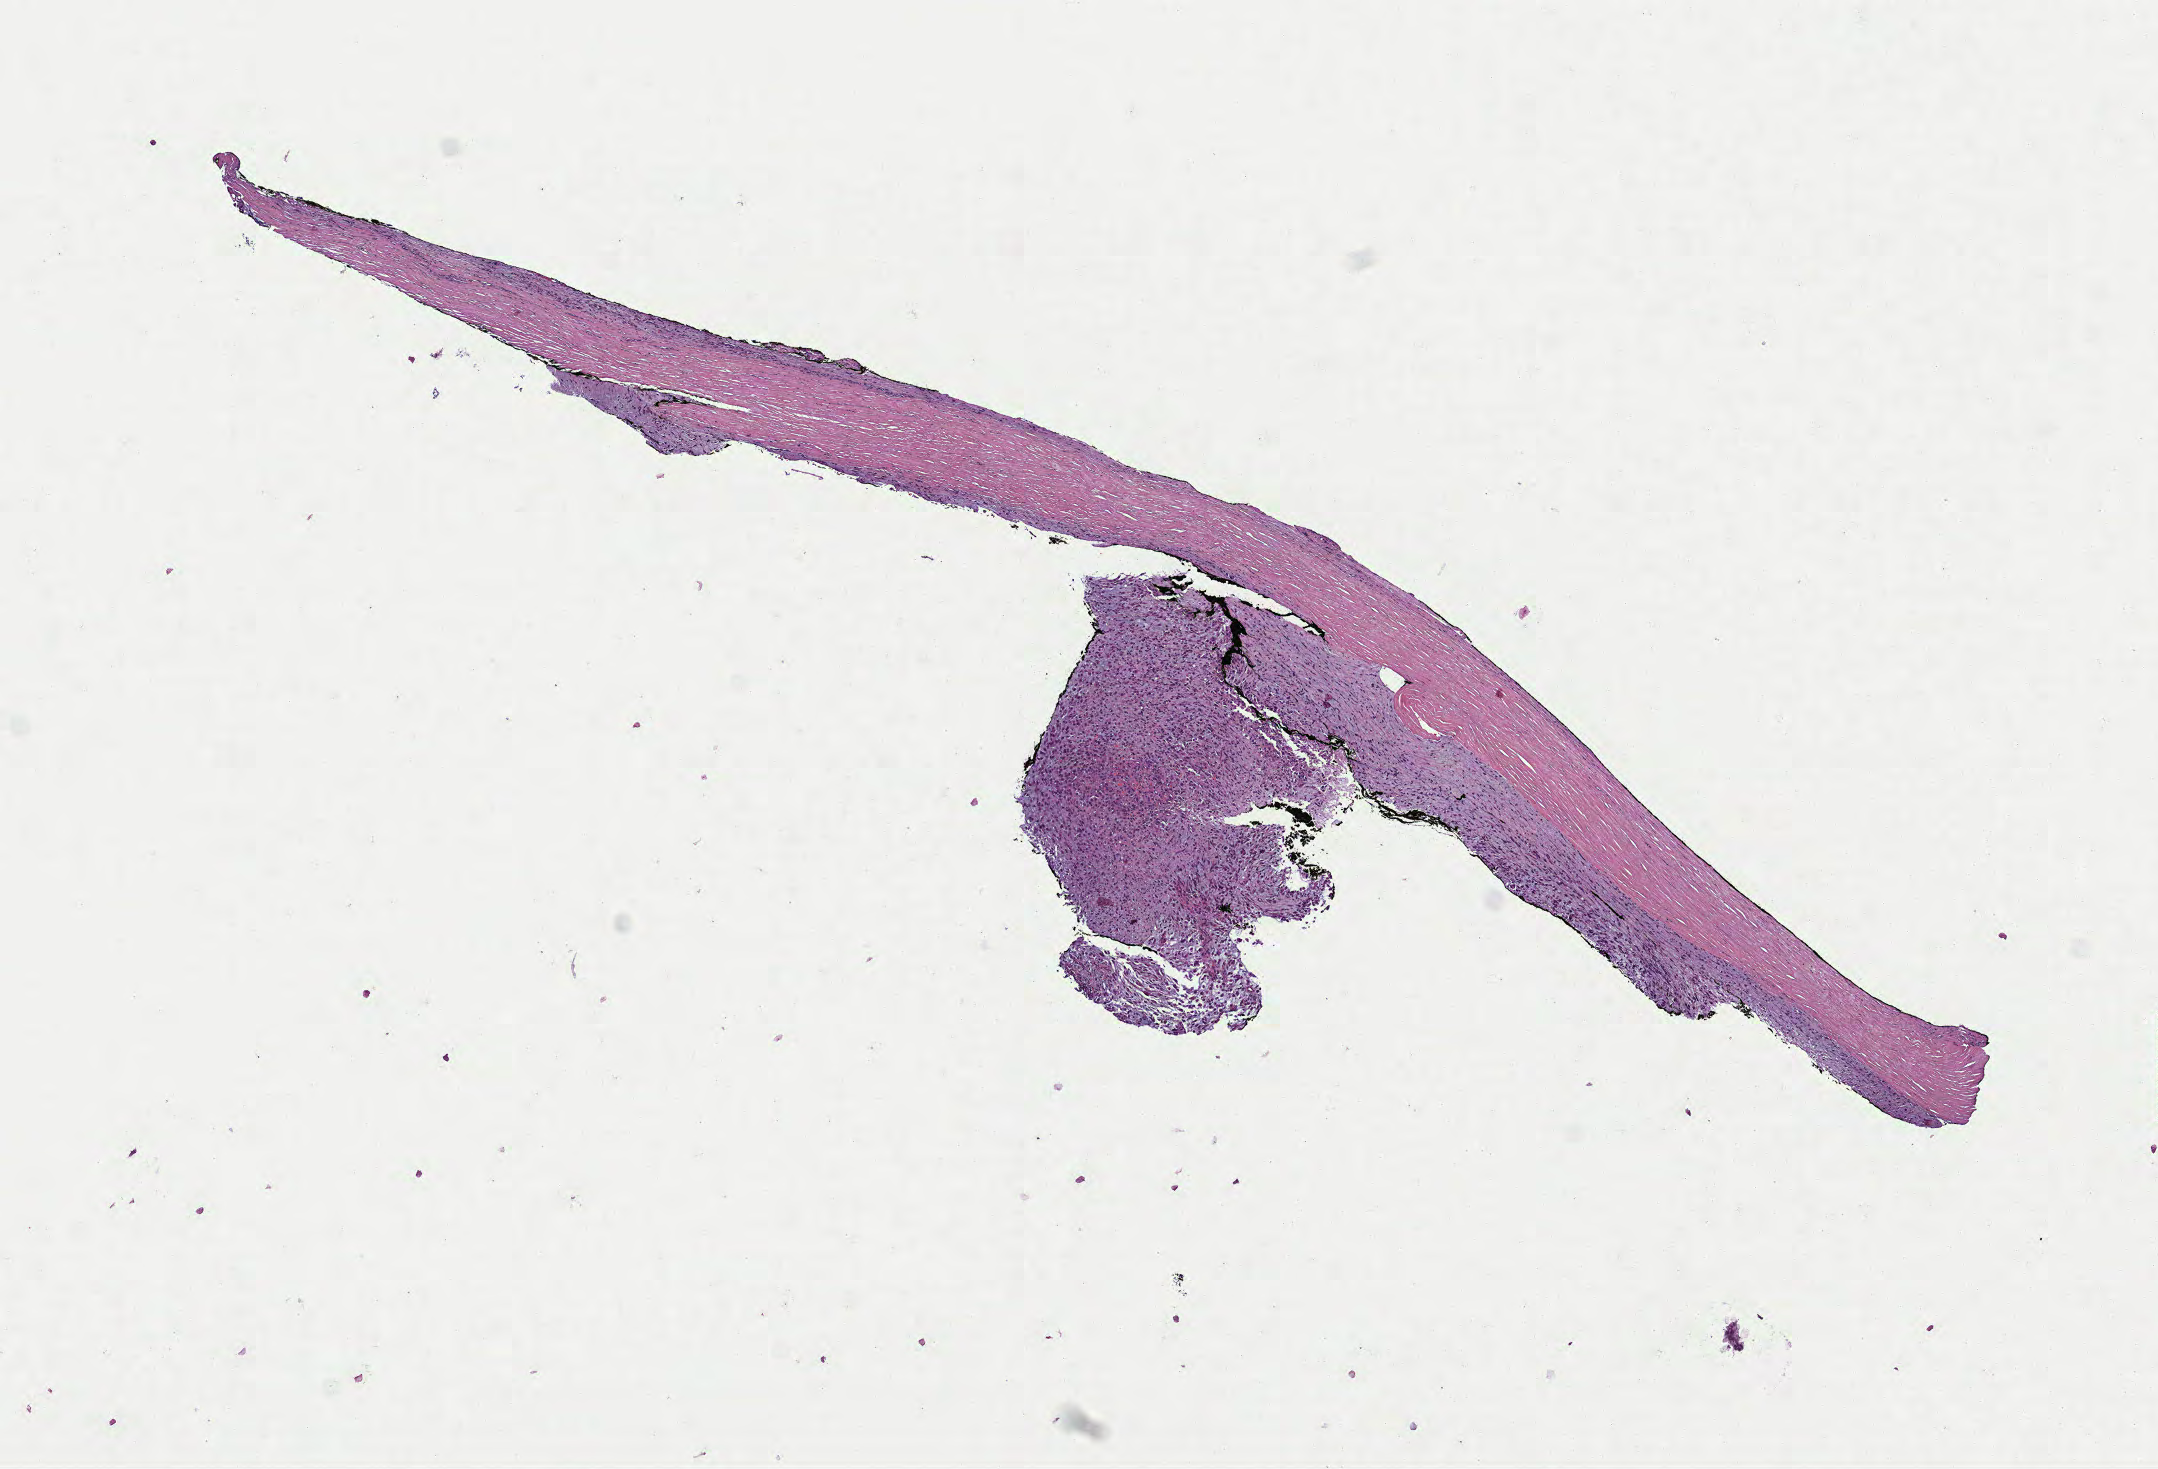
Hematoxylin and eosin (H&E) stained whole-slide image — whole scanned area (about 8.7 x 5.9 mm, from a 40x scan) shown as a low-resolution overview, formalin-fixed paraffin-embedded (FFPE) diagnostic section, primary tumour sample from the mesothelium. Male patient; age at initial diagnosis 71 years.
- AJCC pathologic stage: IB (7th edition)
- diagnosis: Mesothelioma, biphasic, malignant (pleura, NOS)
- TNM: T1b NX MX